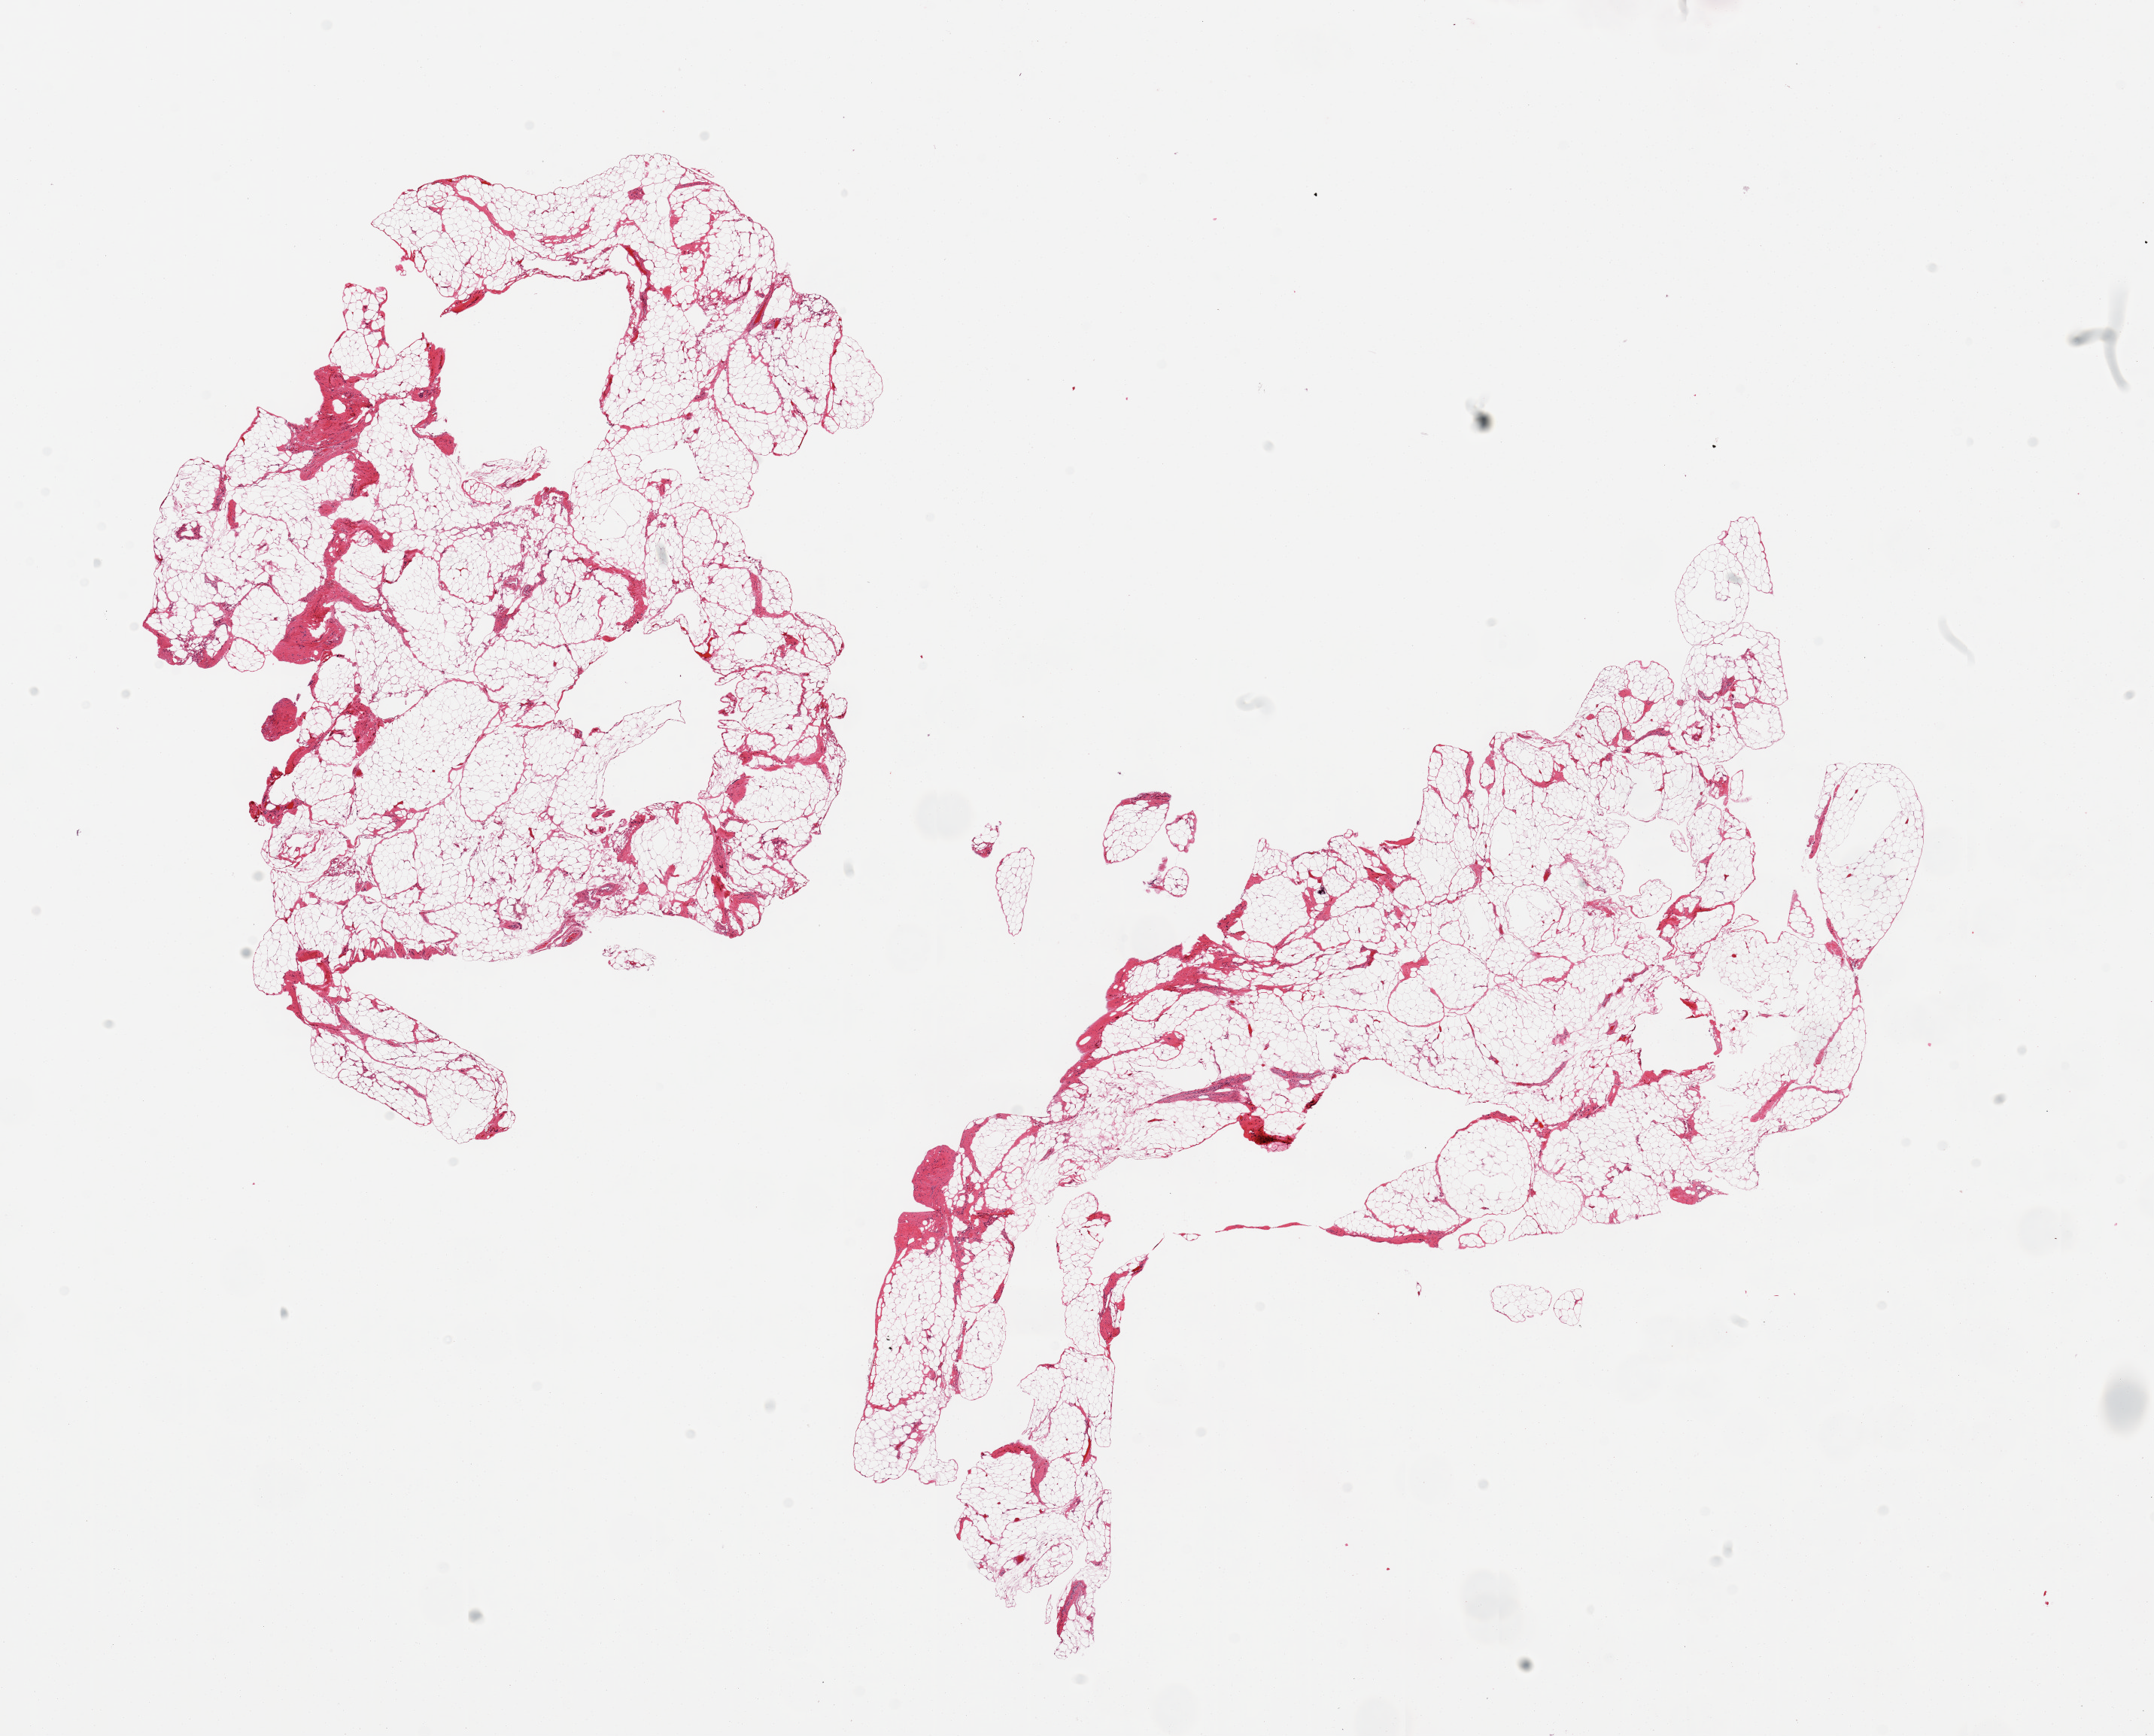
H&E whole-slide image, brightfield, a low-resolution overview of the entire scanned area, about 22.6 x 18.3 mm, PAXgene-fixed, paraffin-embedded tissue, target tissue: omentum, tissue donor sample. Male donor.
• reviewer comment on this tissue sample: 2 pieces